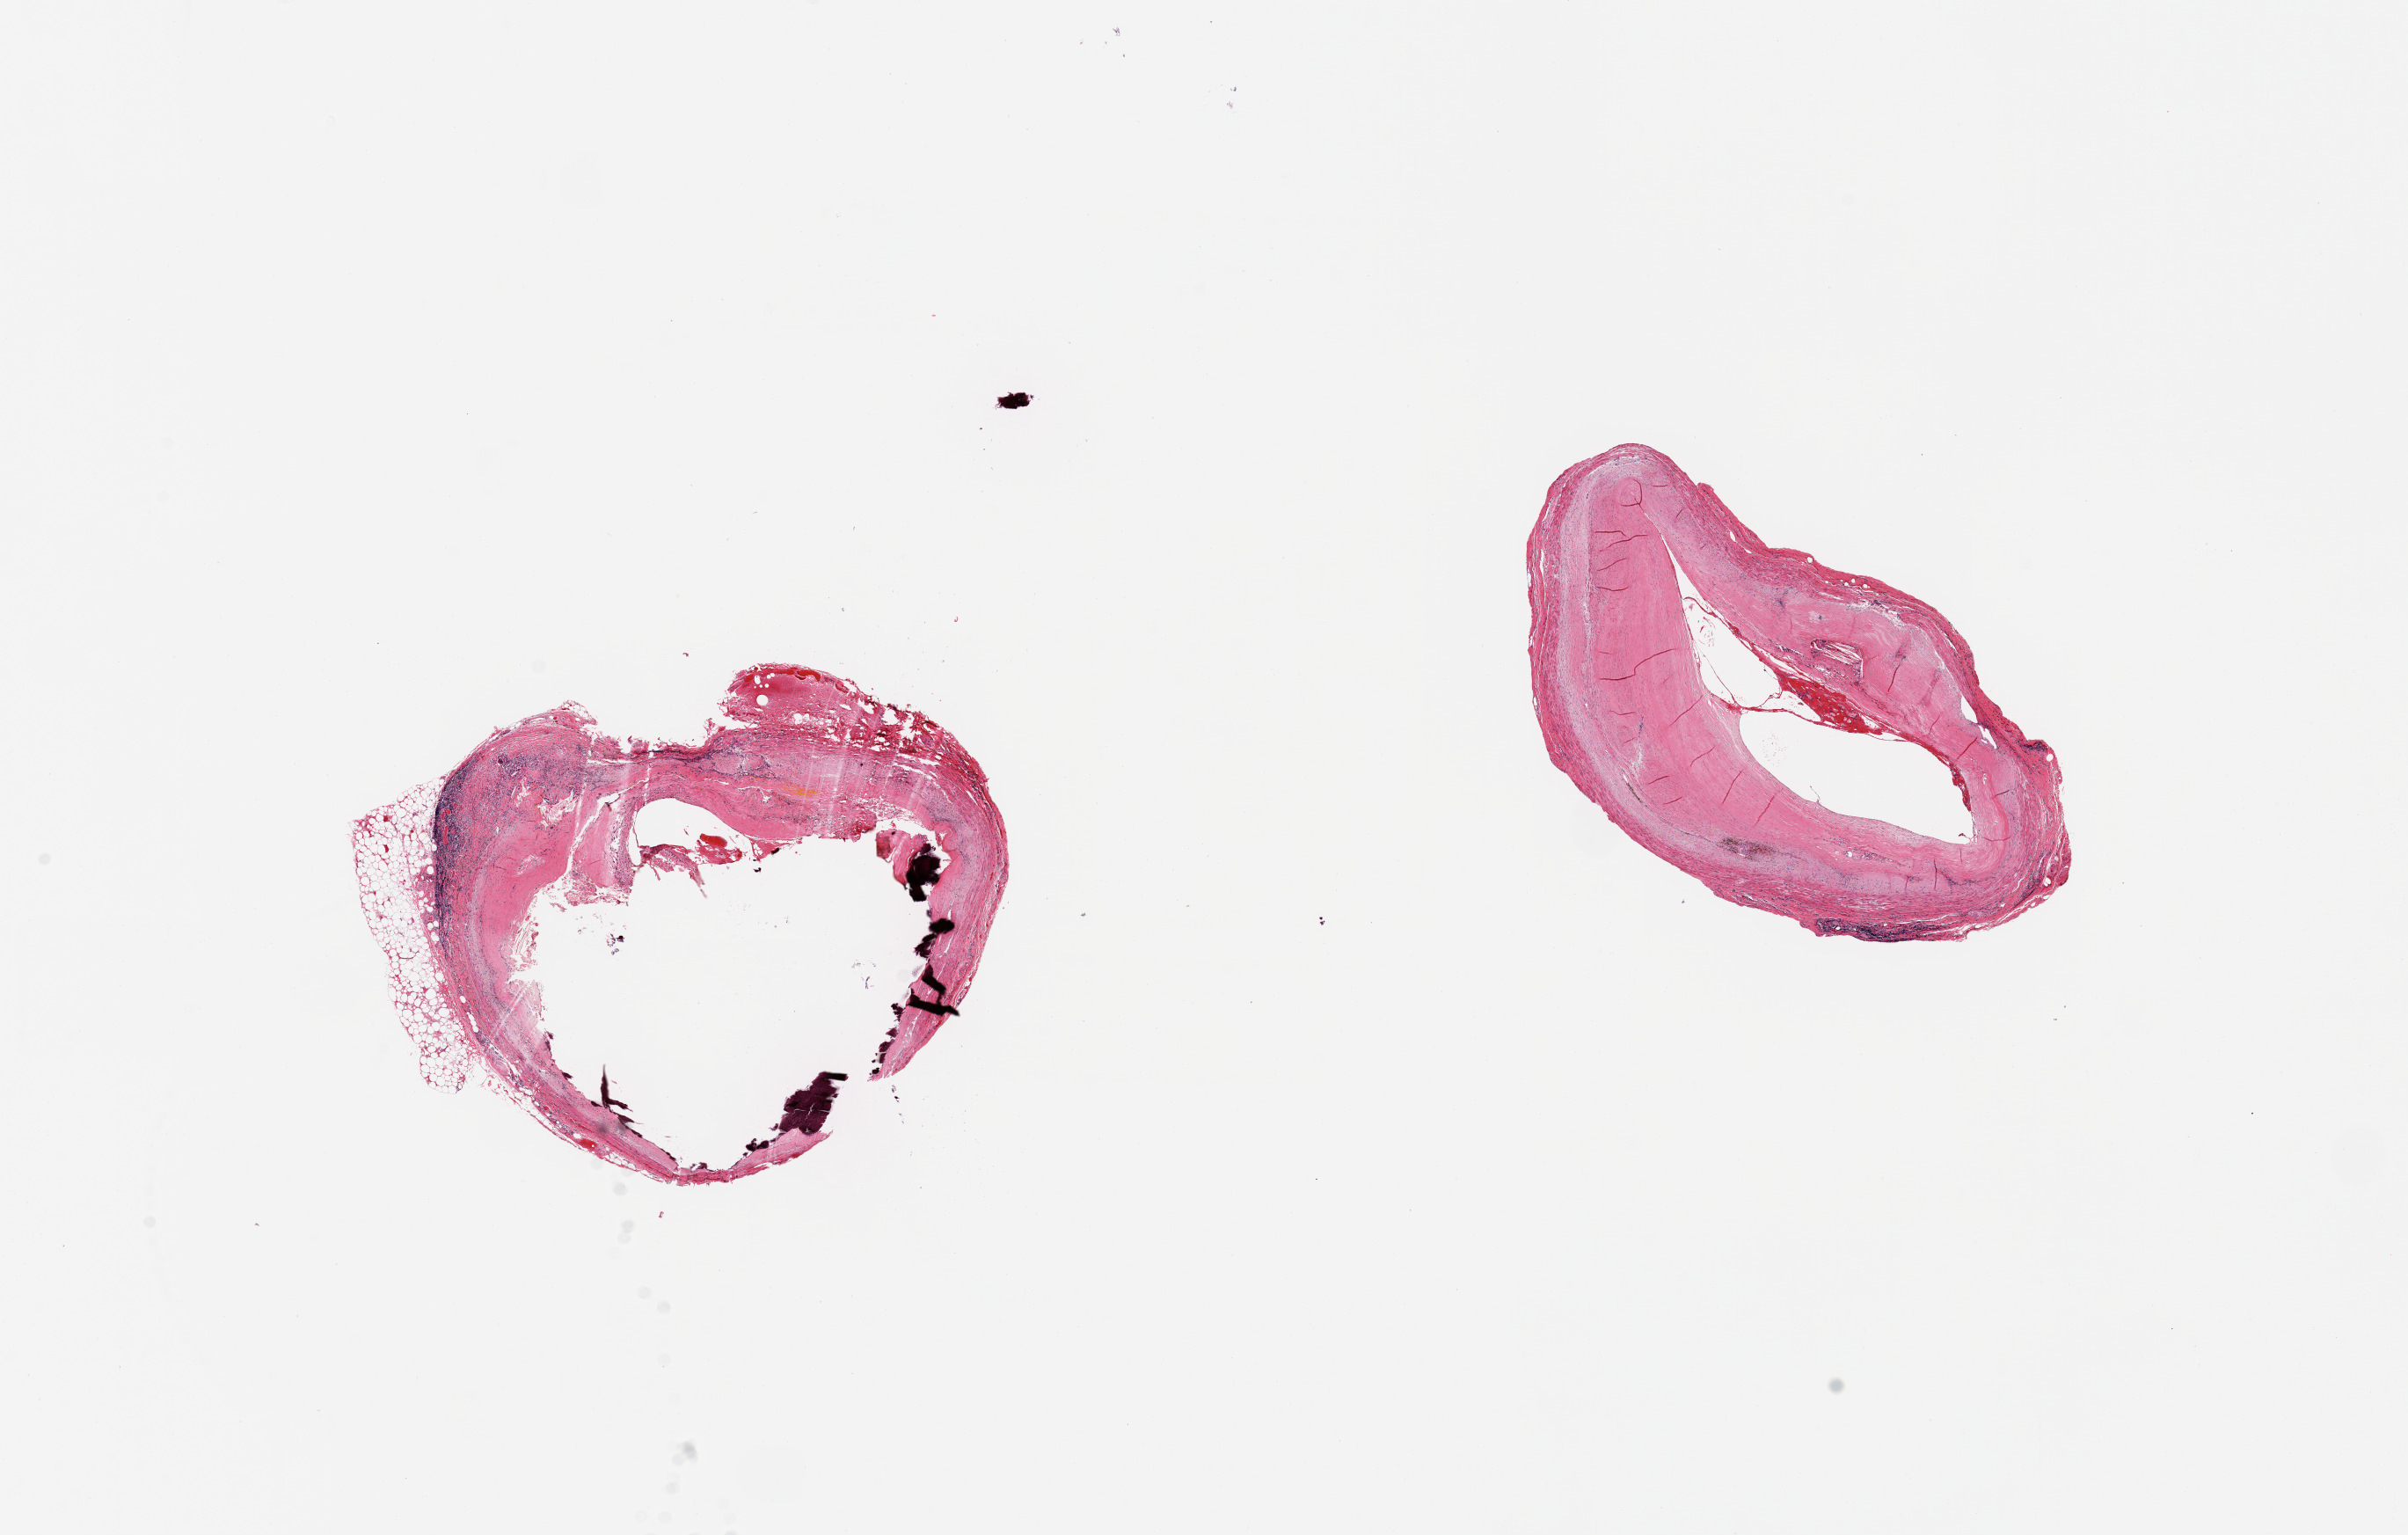
Haematoxylin and eosin whole-slide image, low-resolution overview of the scanned area, about 21.7 x 13.8 mm (acquisition: 20x scan), PAXgene-fixed paraffin-embedded (PFPE) section, sampled site (target tissue): coronary artery, donor tissue sample. Donor sex: male.
Reviewer comment on this tissue sample: 2 pieces, ~70% occlusive atherosis, focally calcified.